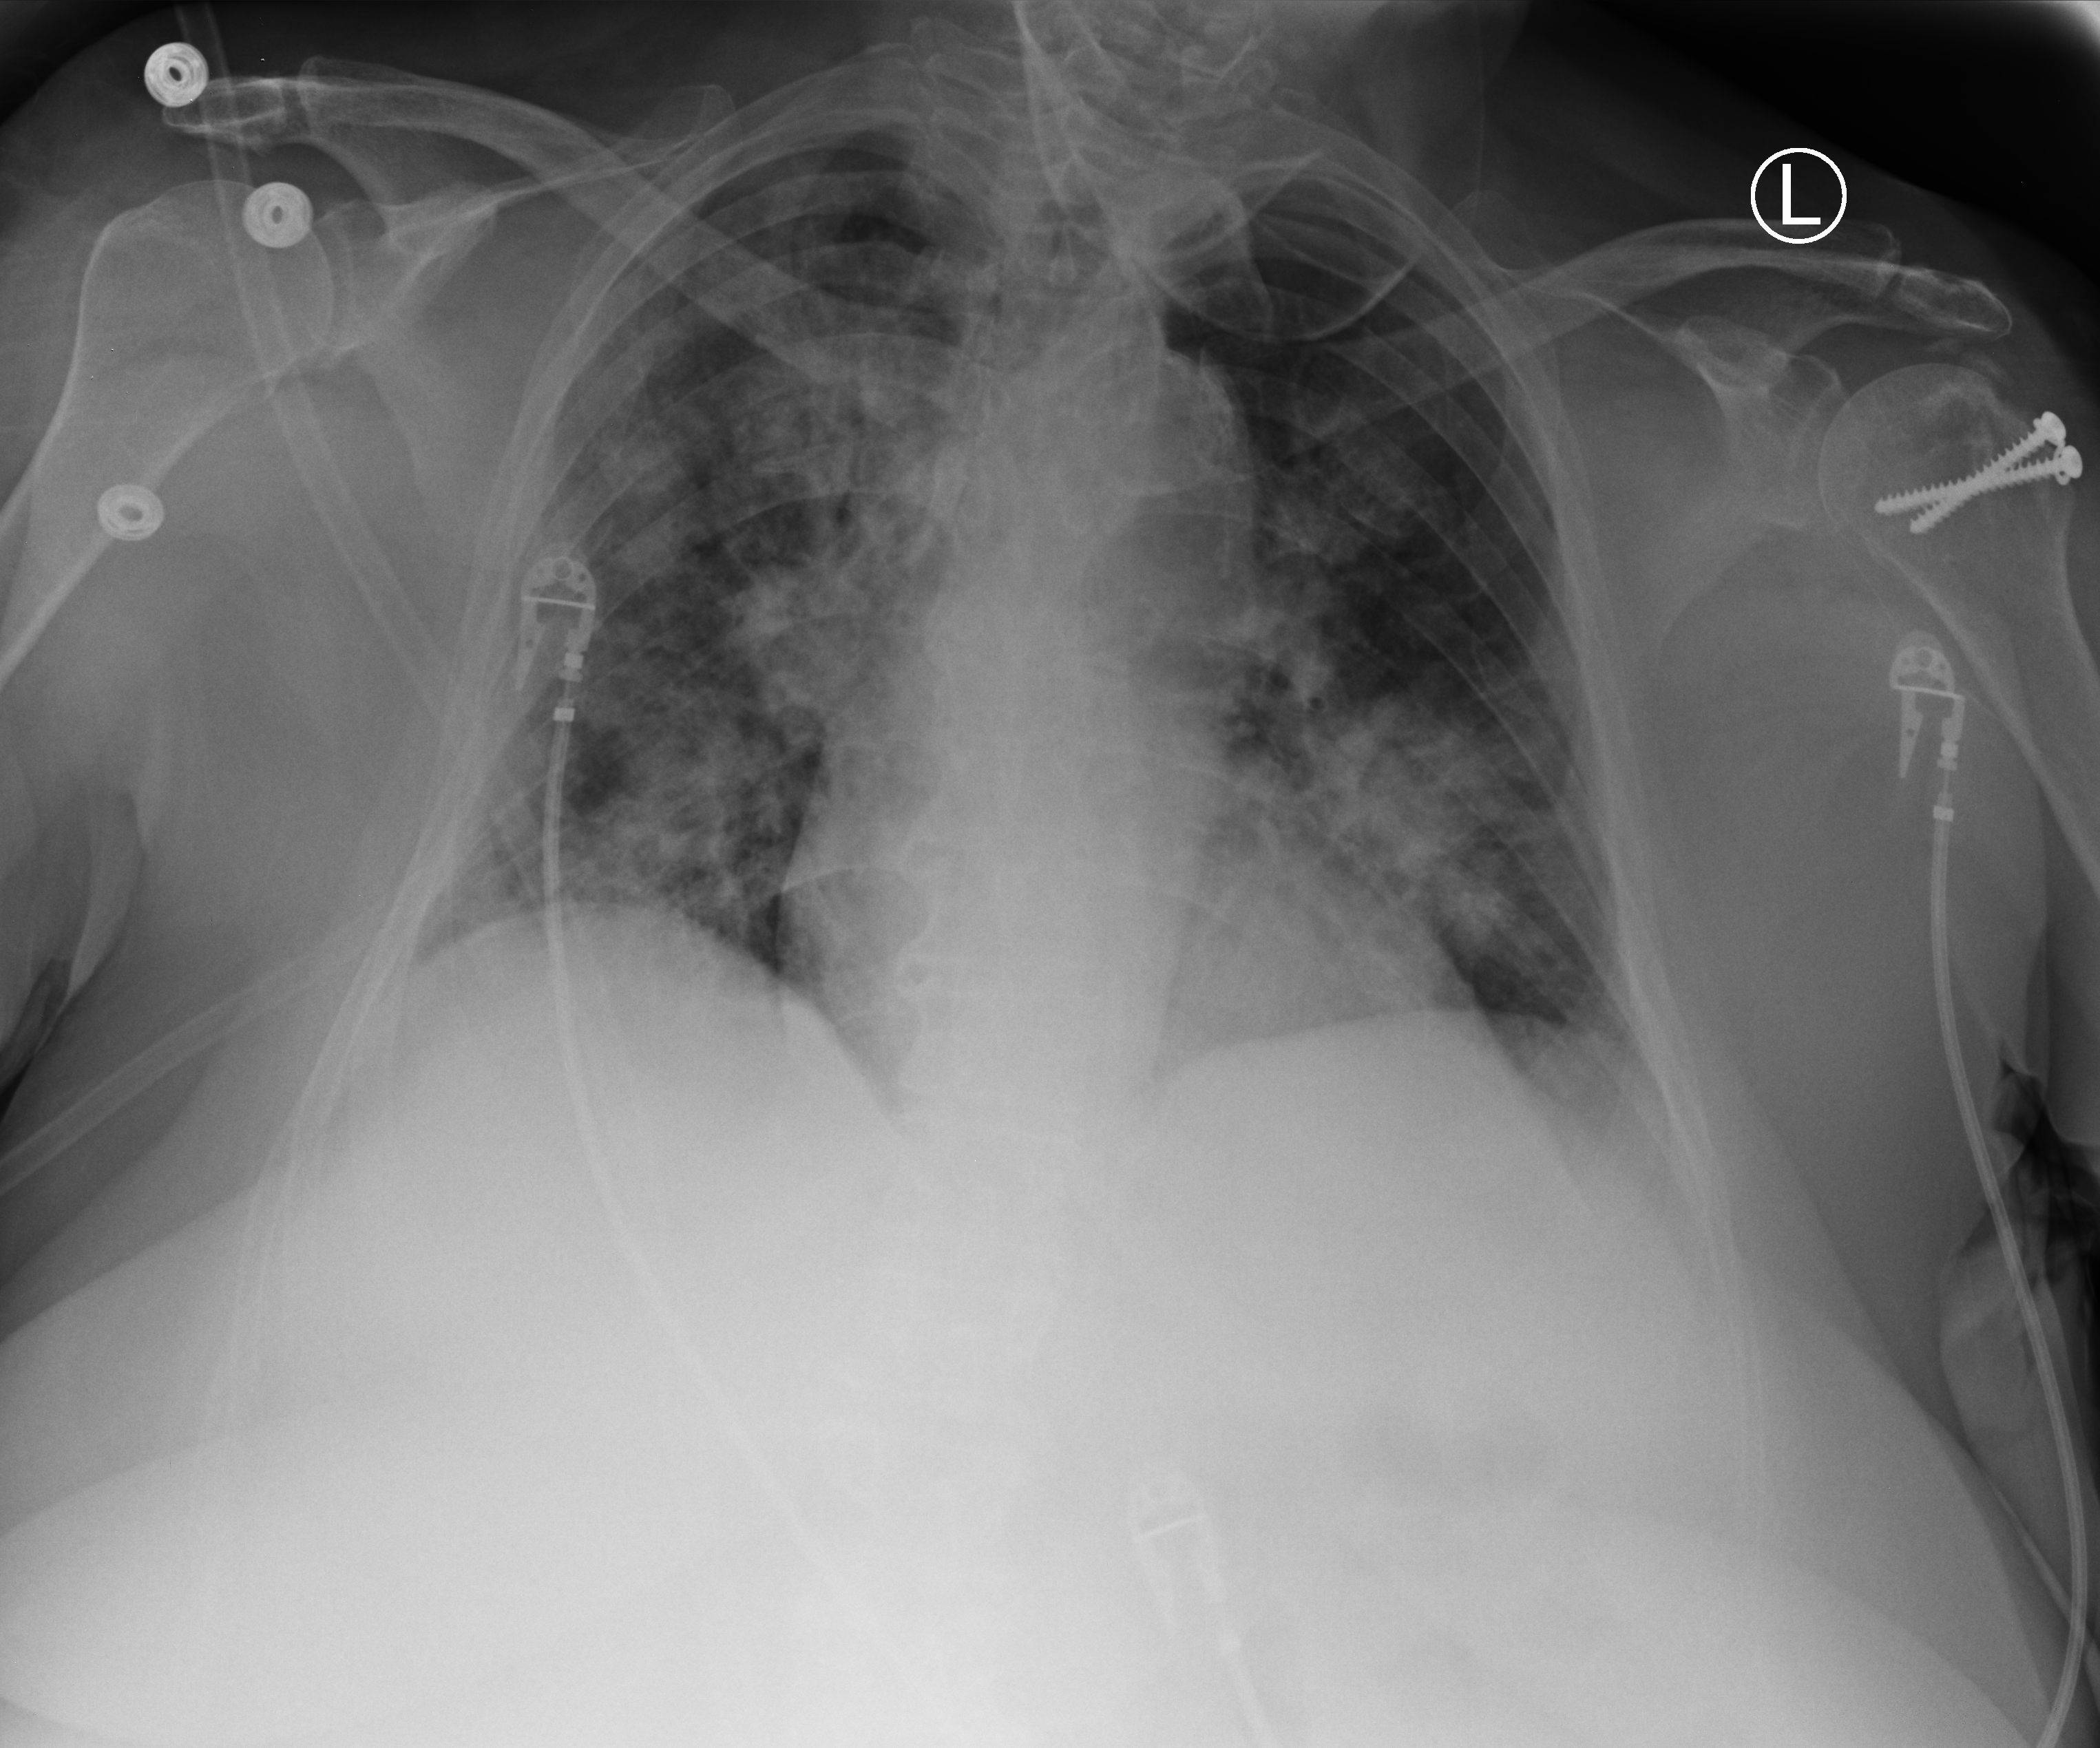
Portable chest radiograph; anteroposterior (AP) projection. Patient hospitalised with COVID-19; female, aged 60–74 years.
Admission-level facts for this patient (not findings on this image; timing relative to this image not recorded): admitted to intensive care during this hospital stay: no; mechanically ventilated during this hospital stay: no.